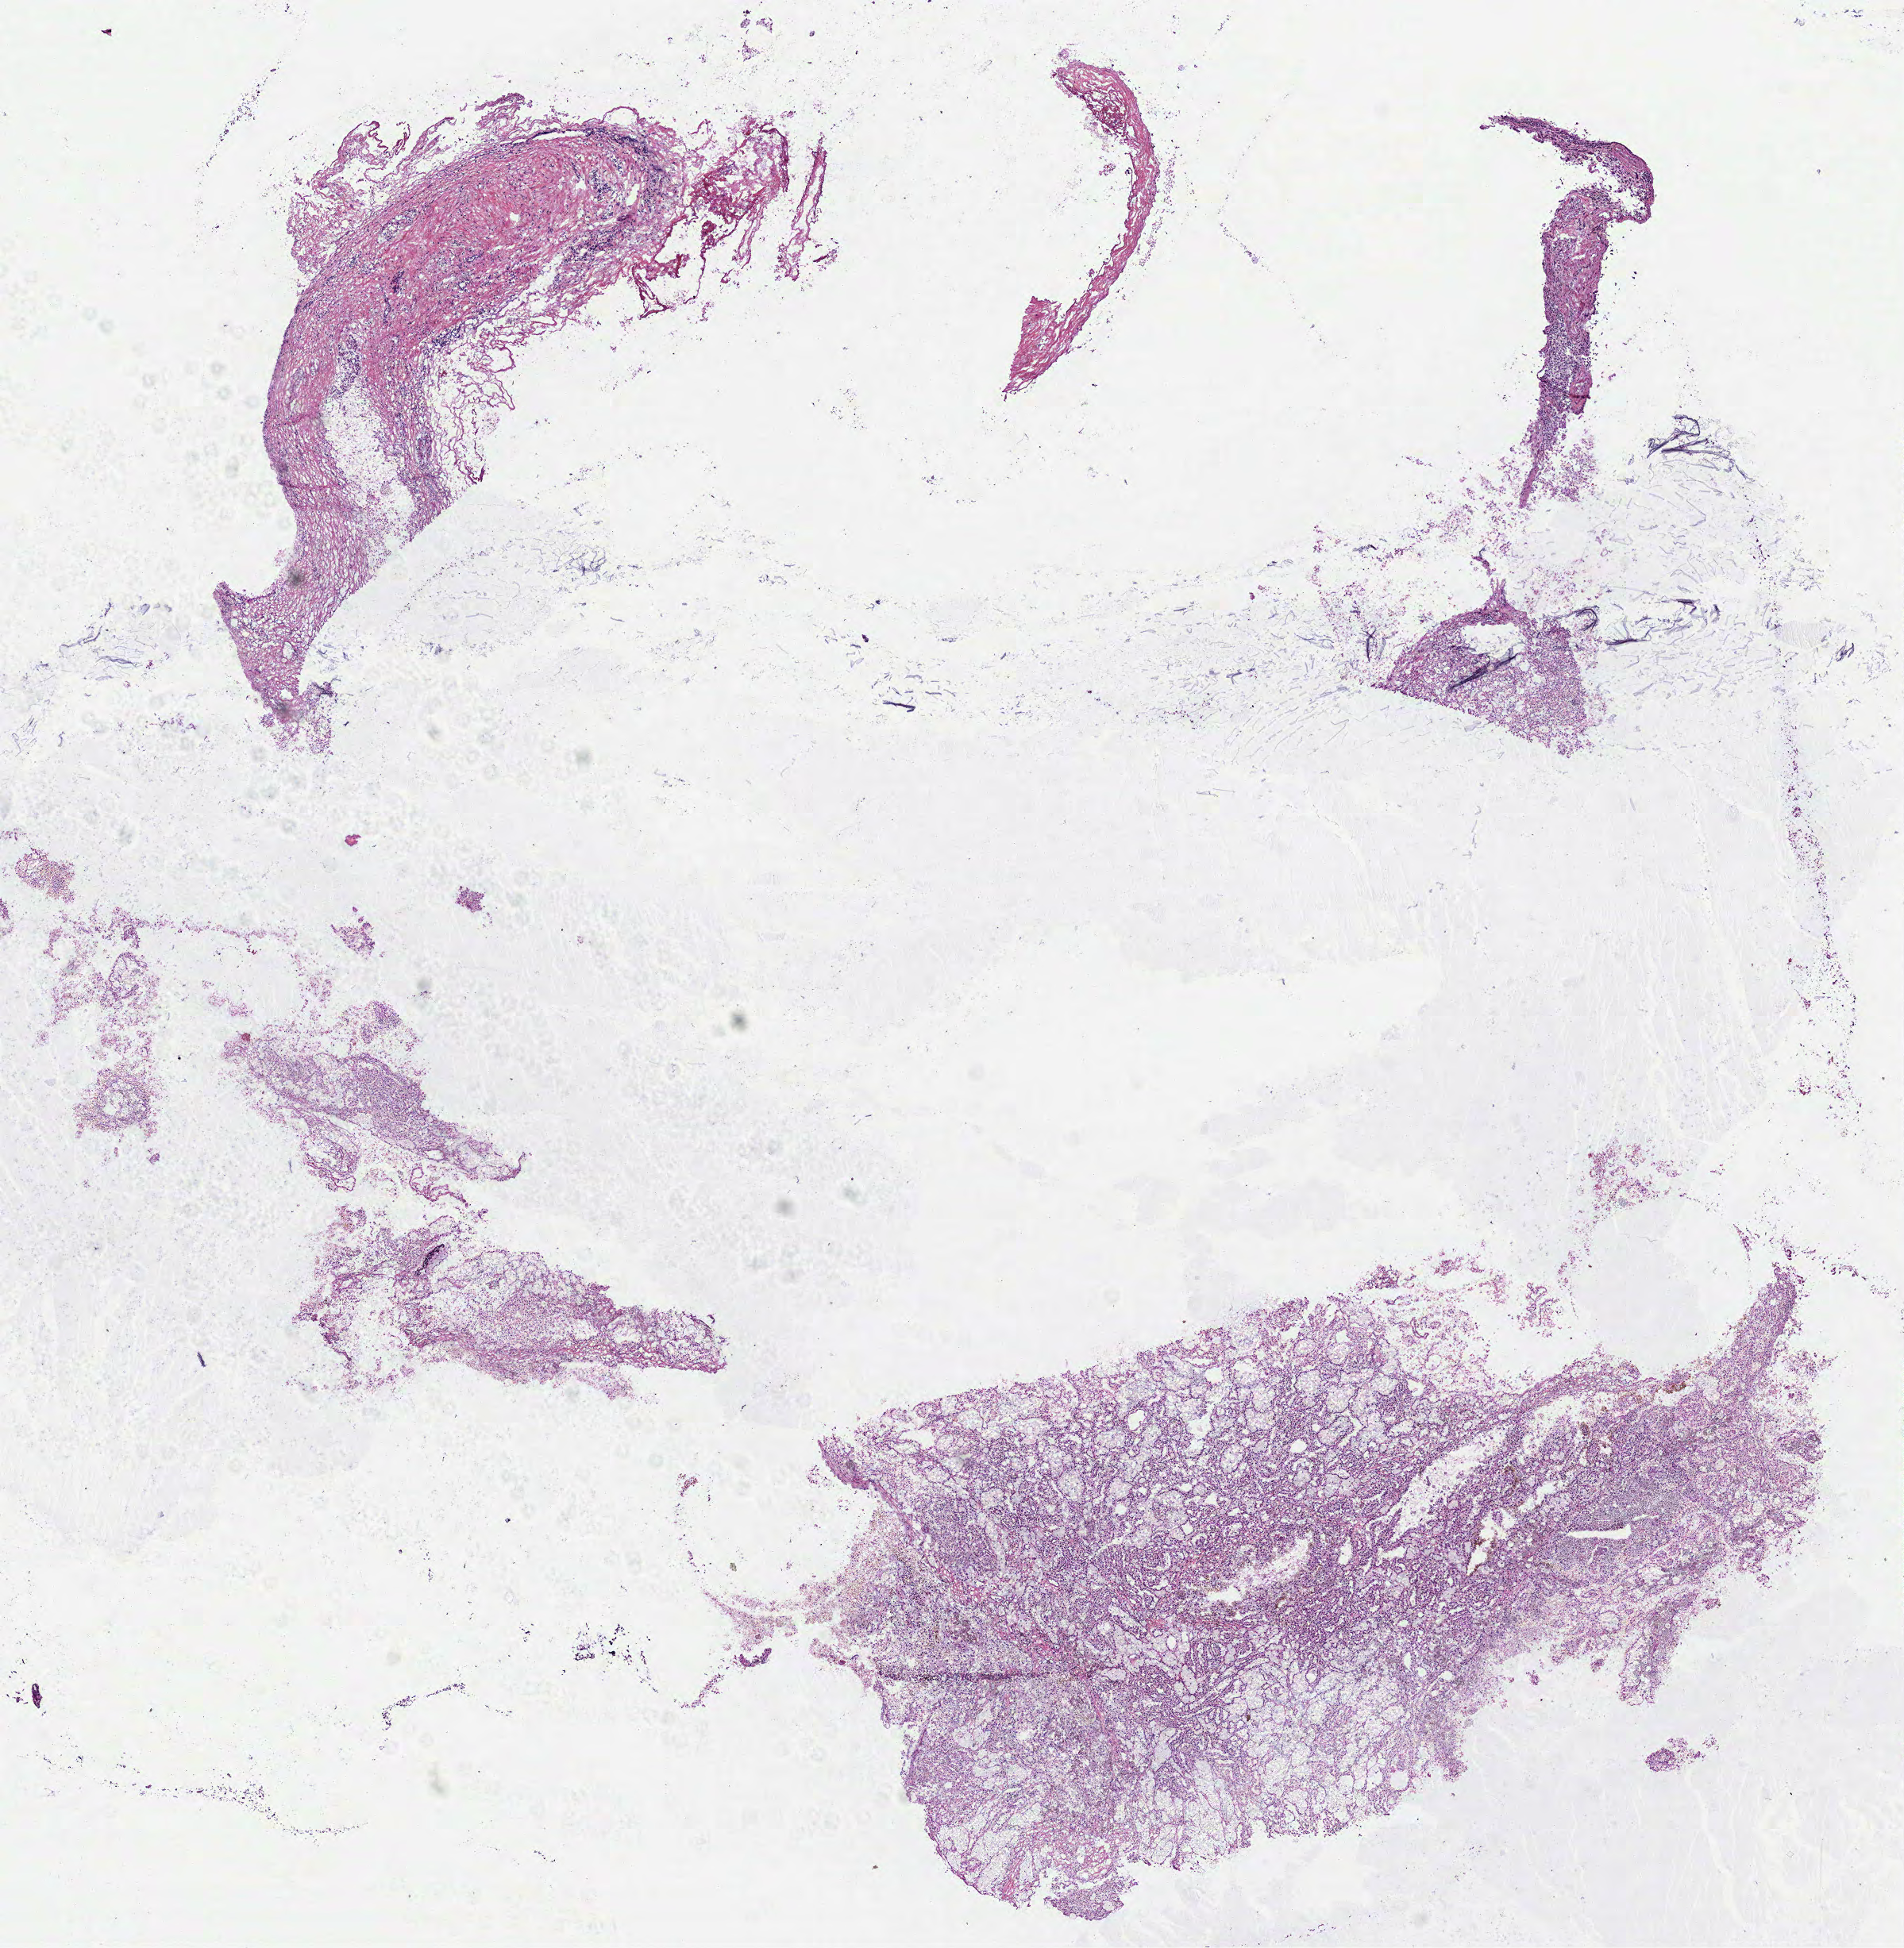
Whole-slide histology image, Hematoxylin and eosin (H&E) stained, whole scanned area (about 9.7 x 9.9 mm, acquisition: 40x scan) shown as a low-resolution overview, frozen section, kidney, primary tumour sample. Male, age 53 years at initial diagnosis. Composition of this section per pathologist review: tumour cells 80%, tumour nuclei 80%.
Diagnosis: Papillary adenocarcinoma, NOS.